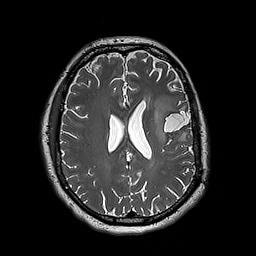
Brain MRI from a brain-tumour surgery series, one axial slice. Position 83 of 192 along the scan axis. 1 mm slice thickness. 256 × 256 image matrix, field of view 250 × 250 mm. From the clinical record (not read from this slice): histopathology: Astrocytoma; WHO grade: 3; IDH mutation: yes; tumour location: Left Insular.
Annotated regions visible in this slice (outlined manually by an expert reader):
- tumour: box from (x=153, y=95) to (x=178, y=145) px